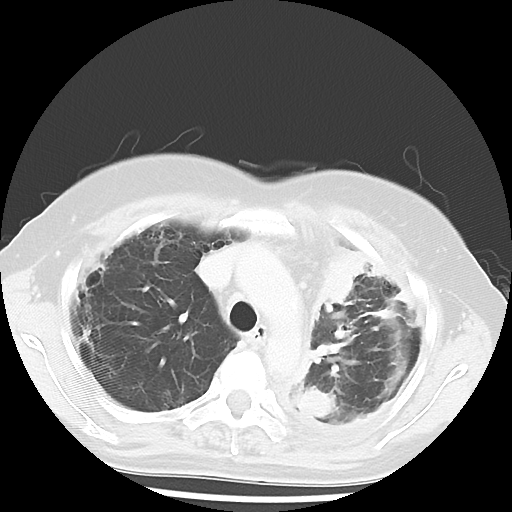
Chest CT, one axial slice; position 41 of 56 along the scan axis; reconstruction kernel LUNG; 120 kVp; lung window (W 1500 / L -600 HU); 5 mm slice thickness; 512 × 512 image matrix. Patient: female, 56 years. Case-level facts recorded for this patient, not image findings: clinical TNM (as recorded): T1c N0 M1.
Outlined on this slice (rectangle marked by the reading radiologist):
- lung tumour (recorded histology: adenocarcinoma): bounding box (x1, y1, x2, y2) in pixels: (313, 241, 360, 319)